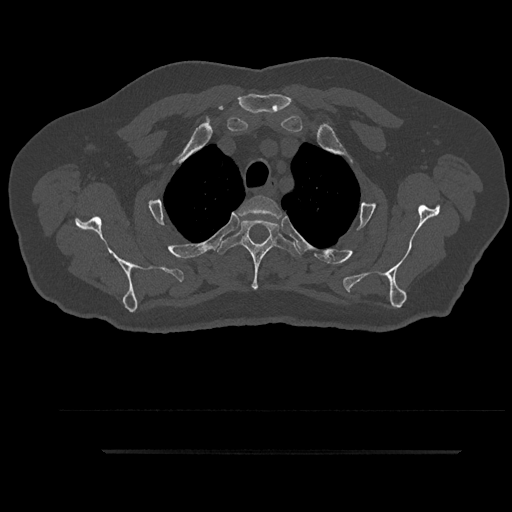
CT including the spine, one axial slice. Slice 726 of 797 in the series (ordered by position). Reconstruction kernel Br40s/3. 120 kVp. Bone window (W 1800 / L 400 HU). 0.5 mm slice thickness. 512 × 512 image matrix, field of view 432 × 432 mm. Patient: male, 63 years. Case-level facts recorded for this patient, not image findings: primary cancer: renal; vertebrae with lytic lesions (as recorded): T8.
Annotated regions visible in this slice (semi-automatic segmentation, software-assisted and operator-edited):
- T2 vertebra: bounding box (x1, y1, x2, y2) in pixels: (238, 195, 282, 218)
- T3 vertebra: (216, 219, 301, 290)